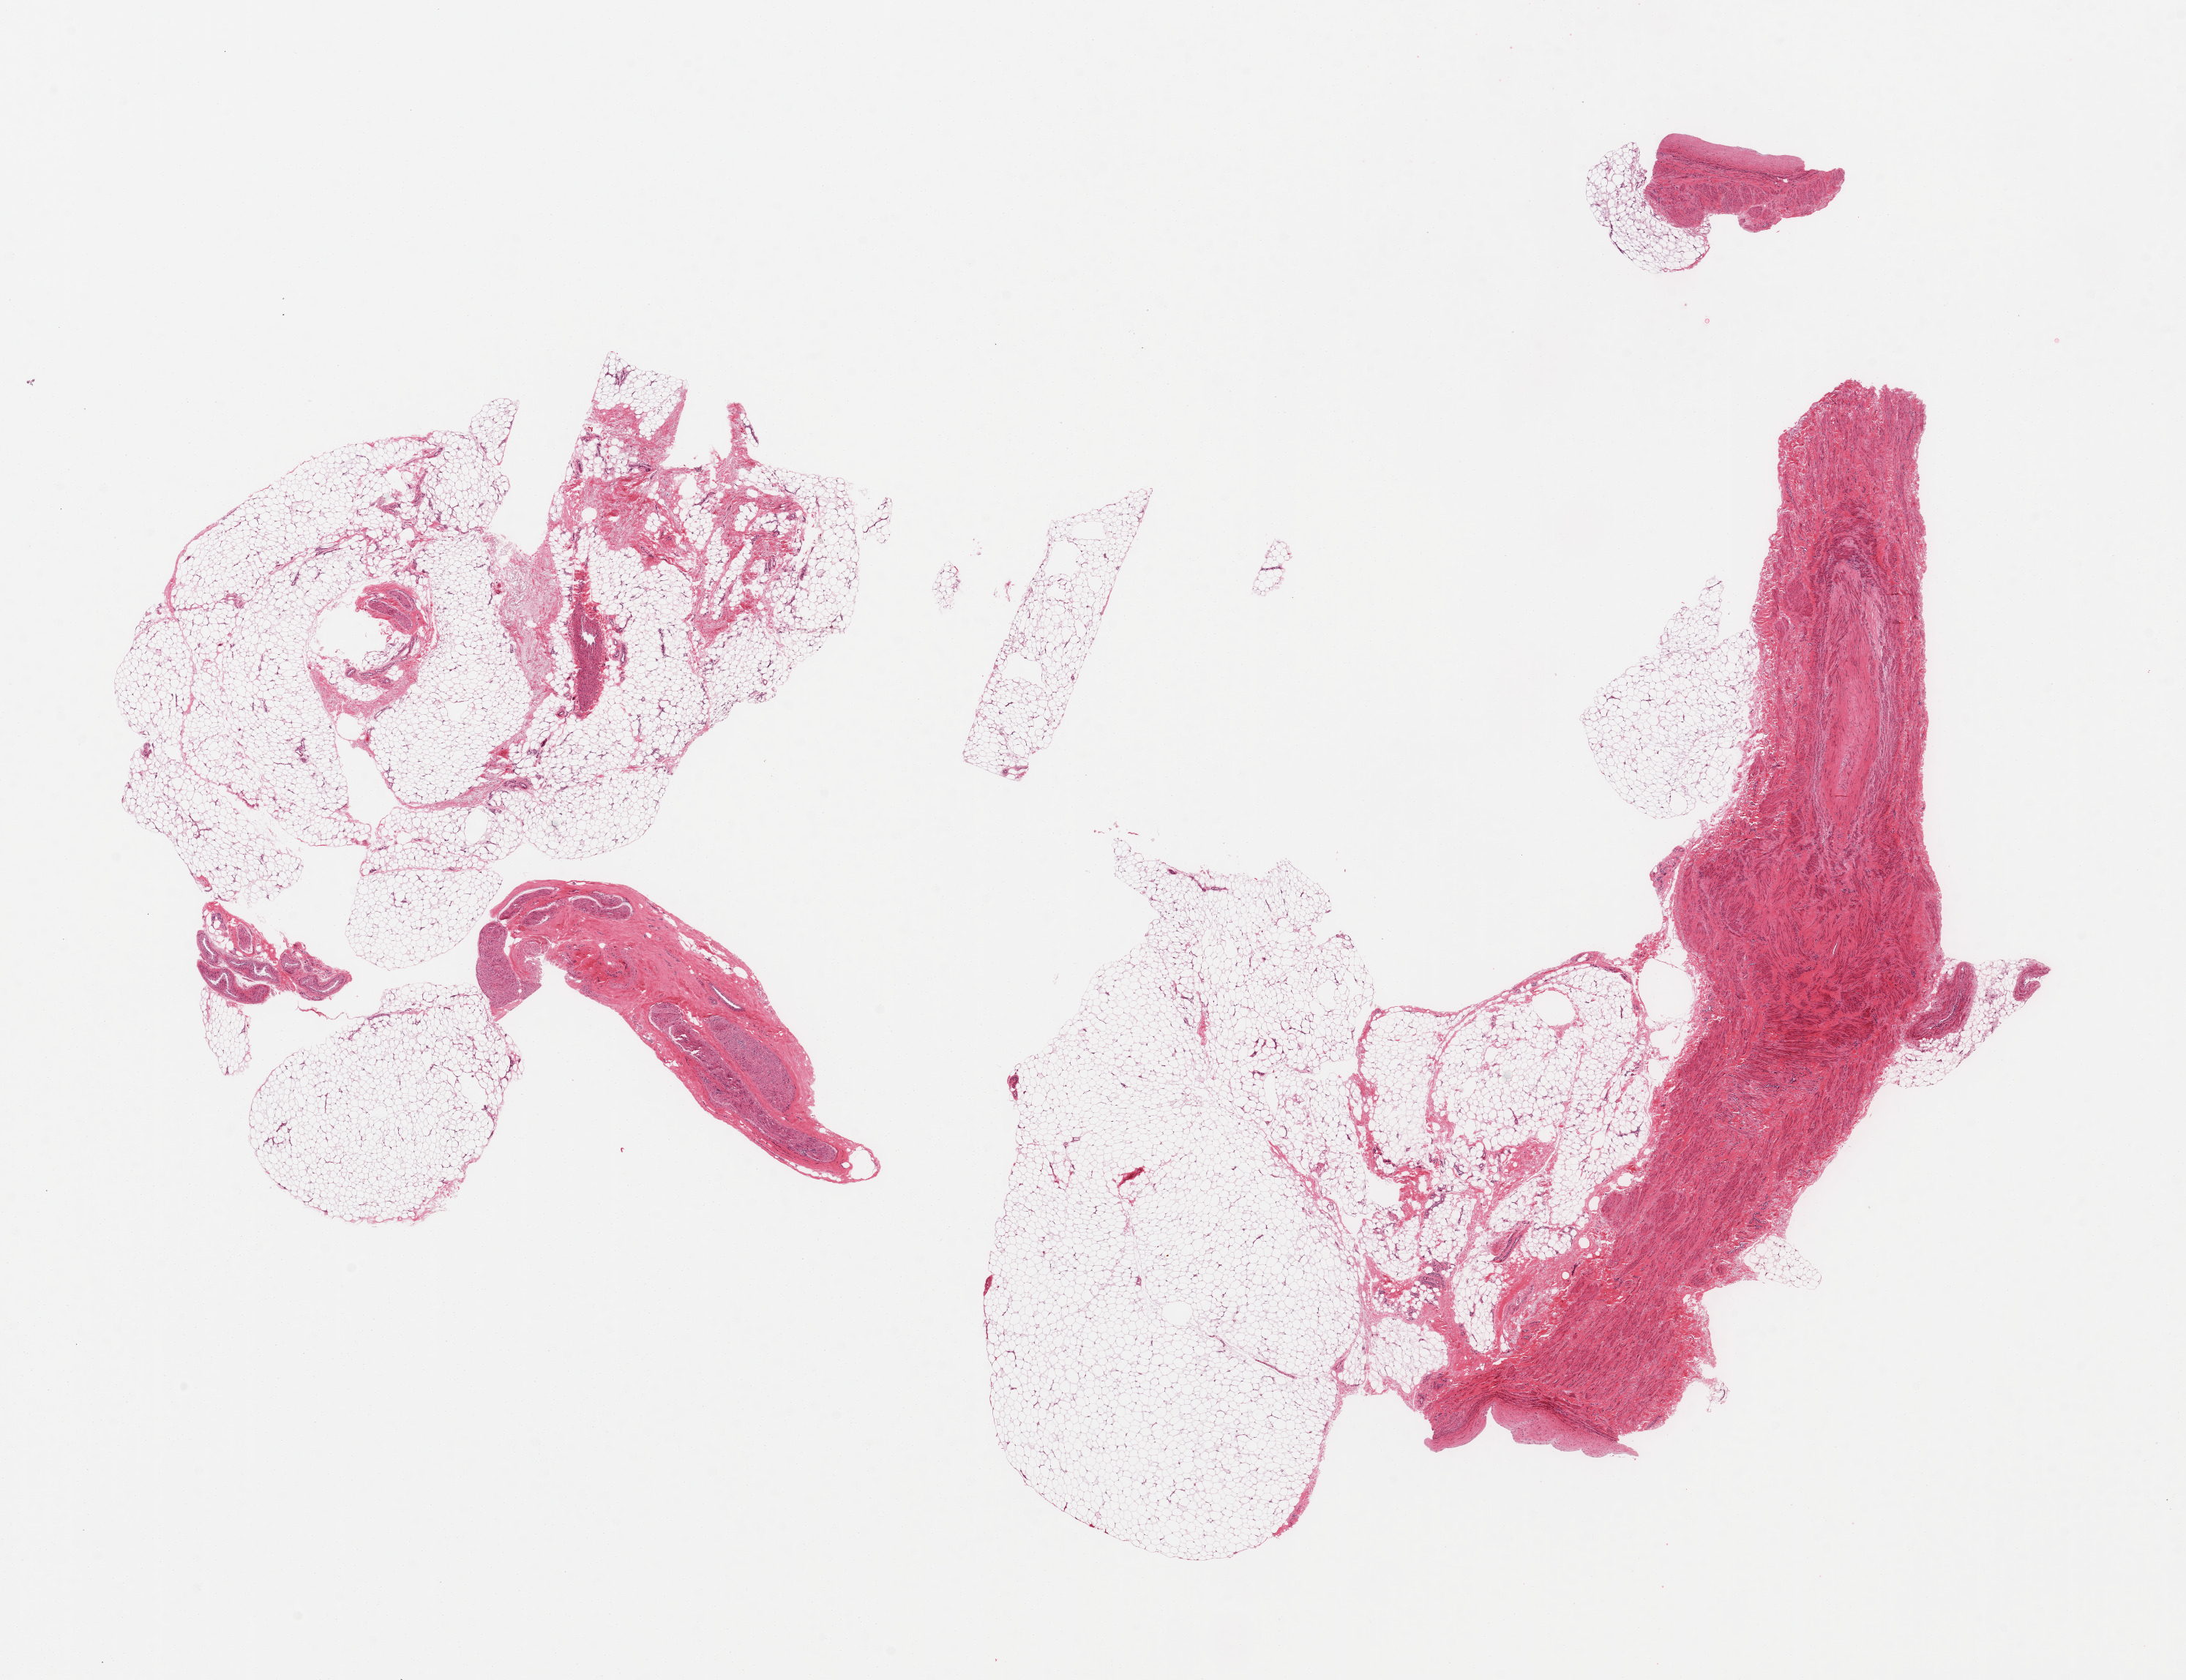
Whole-slide image, hematoxylin and eosin (H&E) stain, a low-resolution overview of the entire scanned area, about 23.6 x 18.2 mm, PAXgene-fixed paraffin-embedded (PFPE) section, target tissue: adipose tissue, donor tissue sample. Donor: male.
• review note (as recorded): 2 pieces, ~40% fascia/peripheral nerve